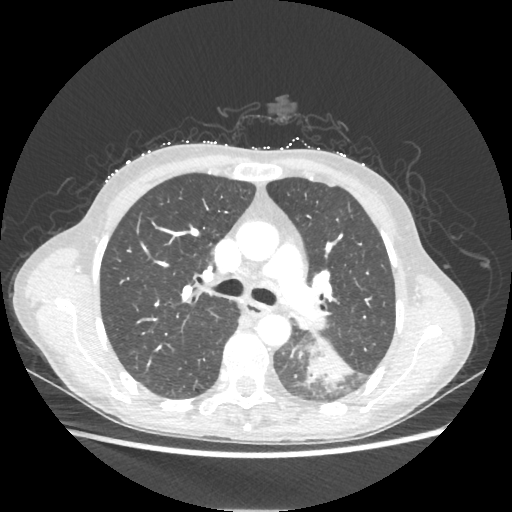
Chest CT, one axial slice; position 139 of 221 along the scan axis; reconstruction kernel STANDARD; 80 kVp; lung window (W 1500 / L -600 HU); 512 × 512 image matrix, field of view 360 × 360 mm. Patient: female, 53 years. From the clinical record (not read from this slice): clinical TNM (as recorded): T3 N0 M0.
Outlined on this slice (rectangle marked by the reading radiologist):
- lung tumour (recorded histology: adenocarcinoma): bounding box <305,340,350,383> (left, top, right, bottom; pixels)